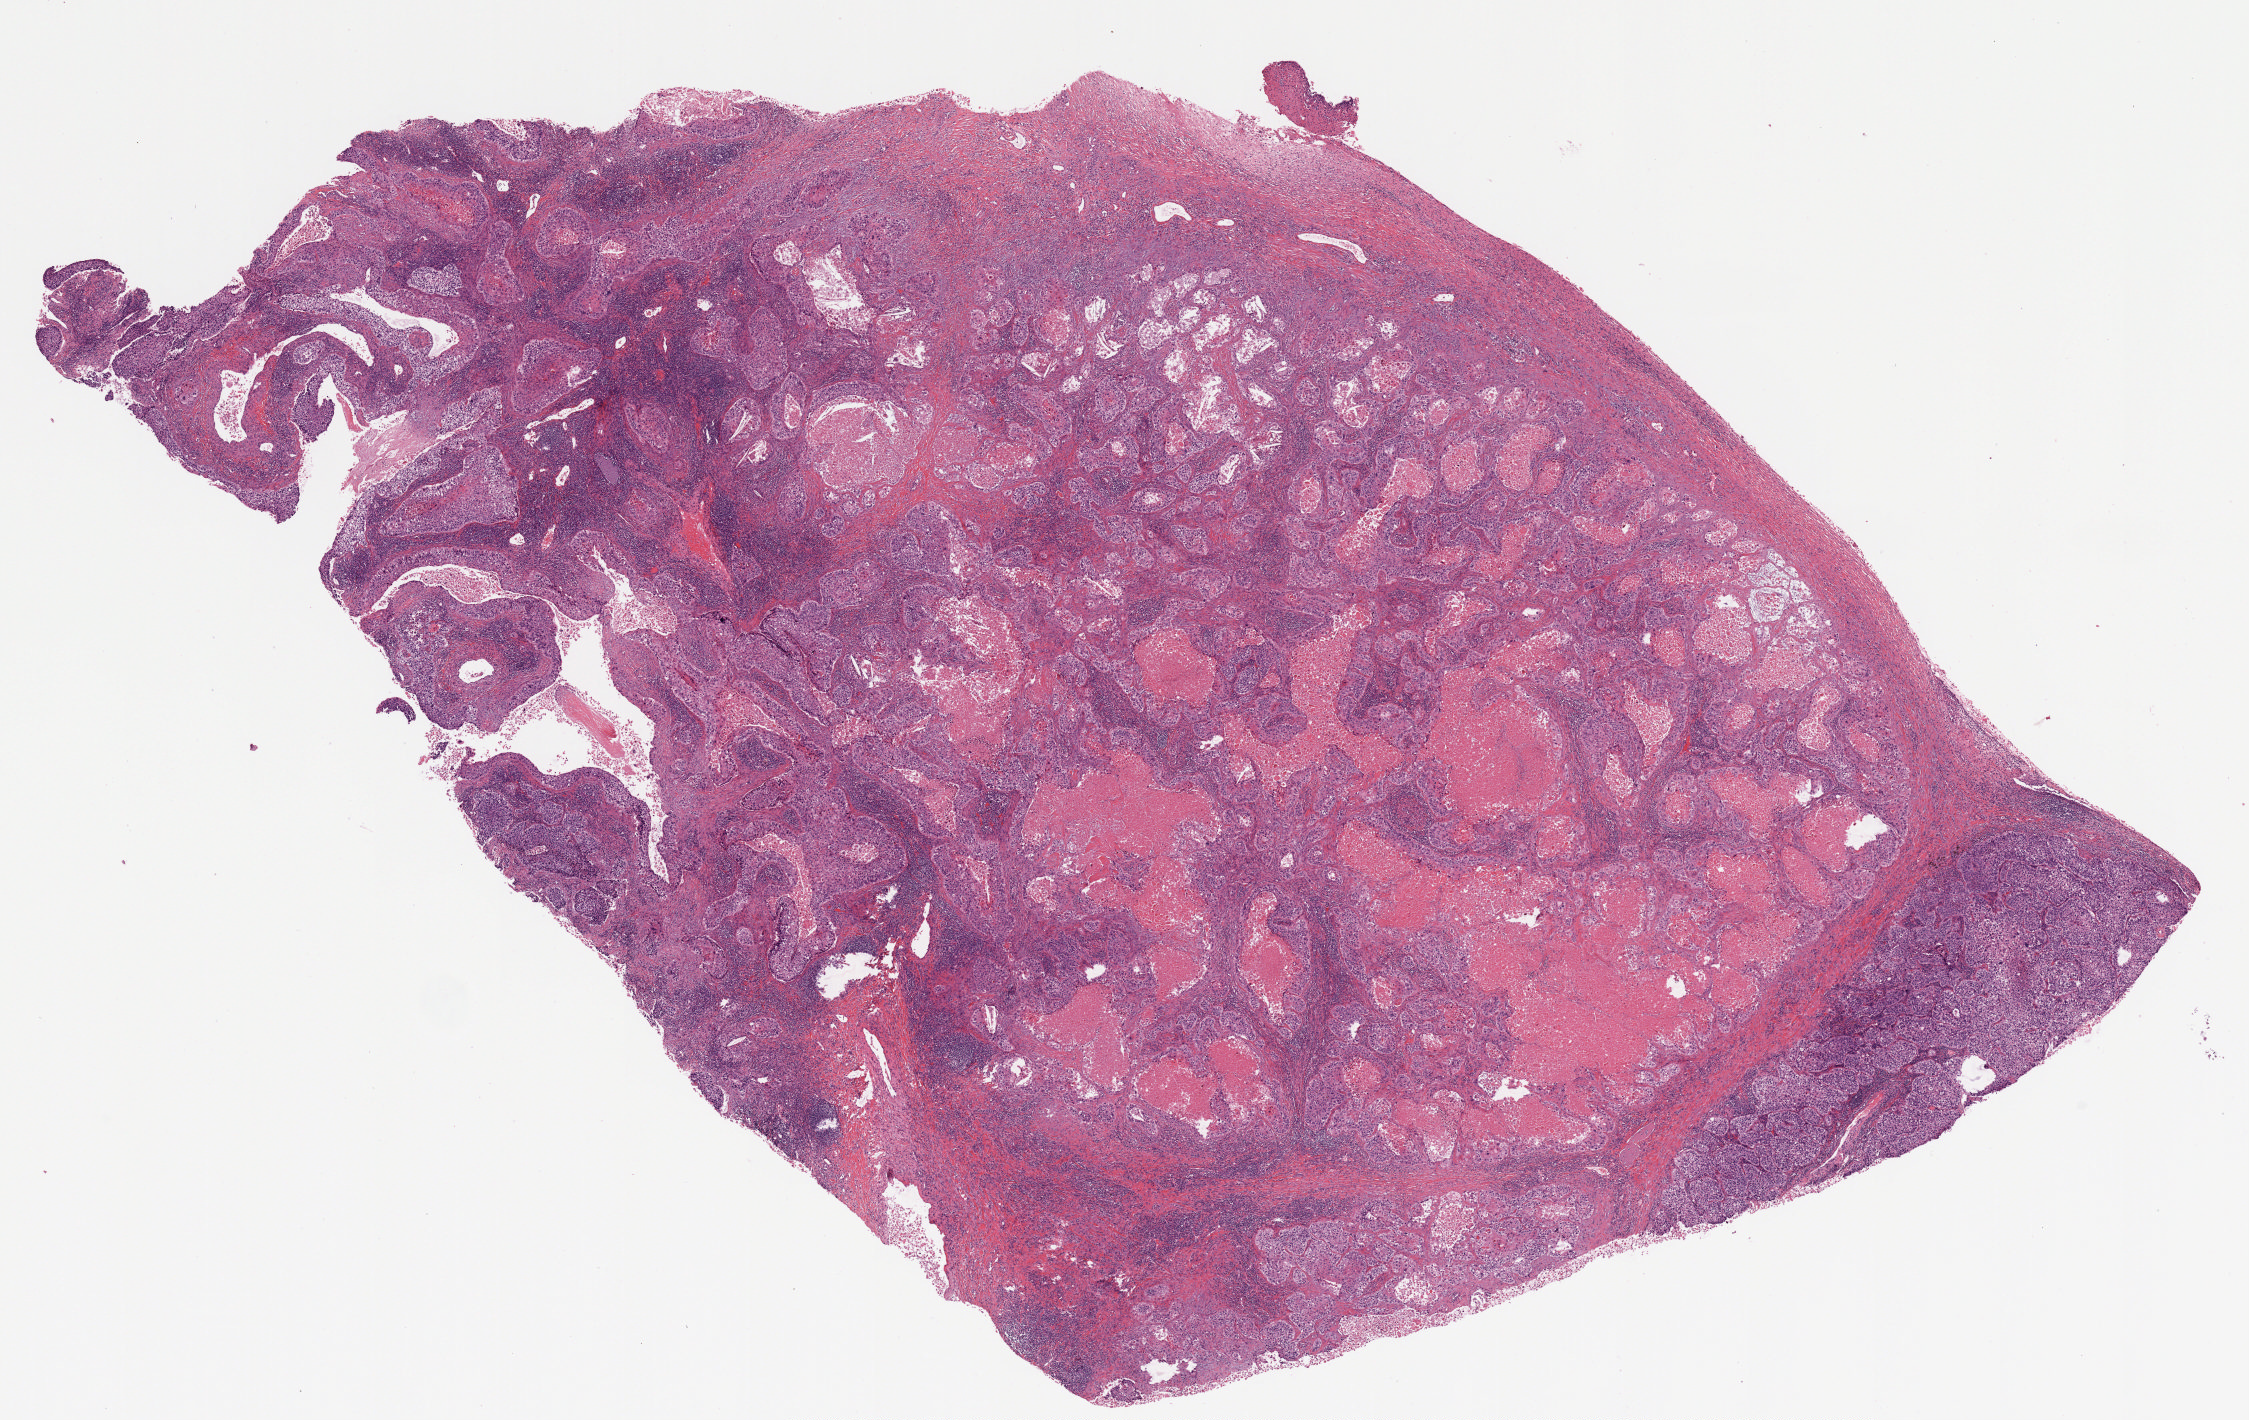
H&E-stained whole-slide image, low-resolution overview of the scanned area, about 18.0 x 11.4 mm (slide scanned at 20x), FFPE section, primary tumour sample from the lung. Male, age 69 years at initial diagnosis.
* histologic diagnosis: Squamous cell carcinoma, NOS (lower lobe, lung)
* AJCC pathologic stage: IIA (7th edition)
* laterality: right